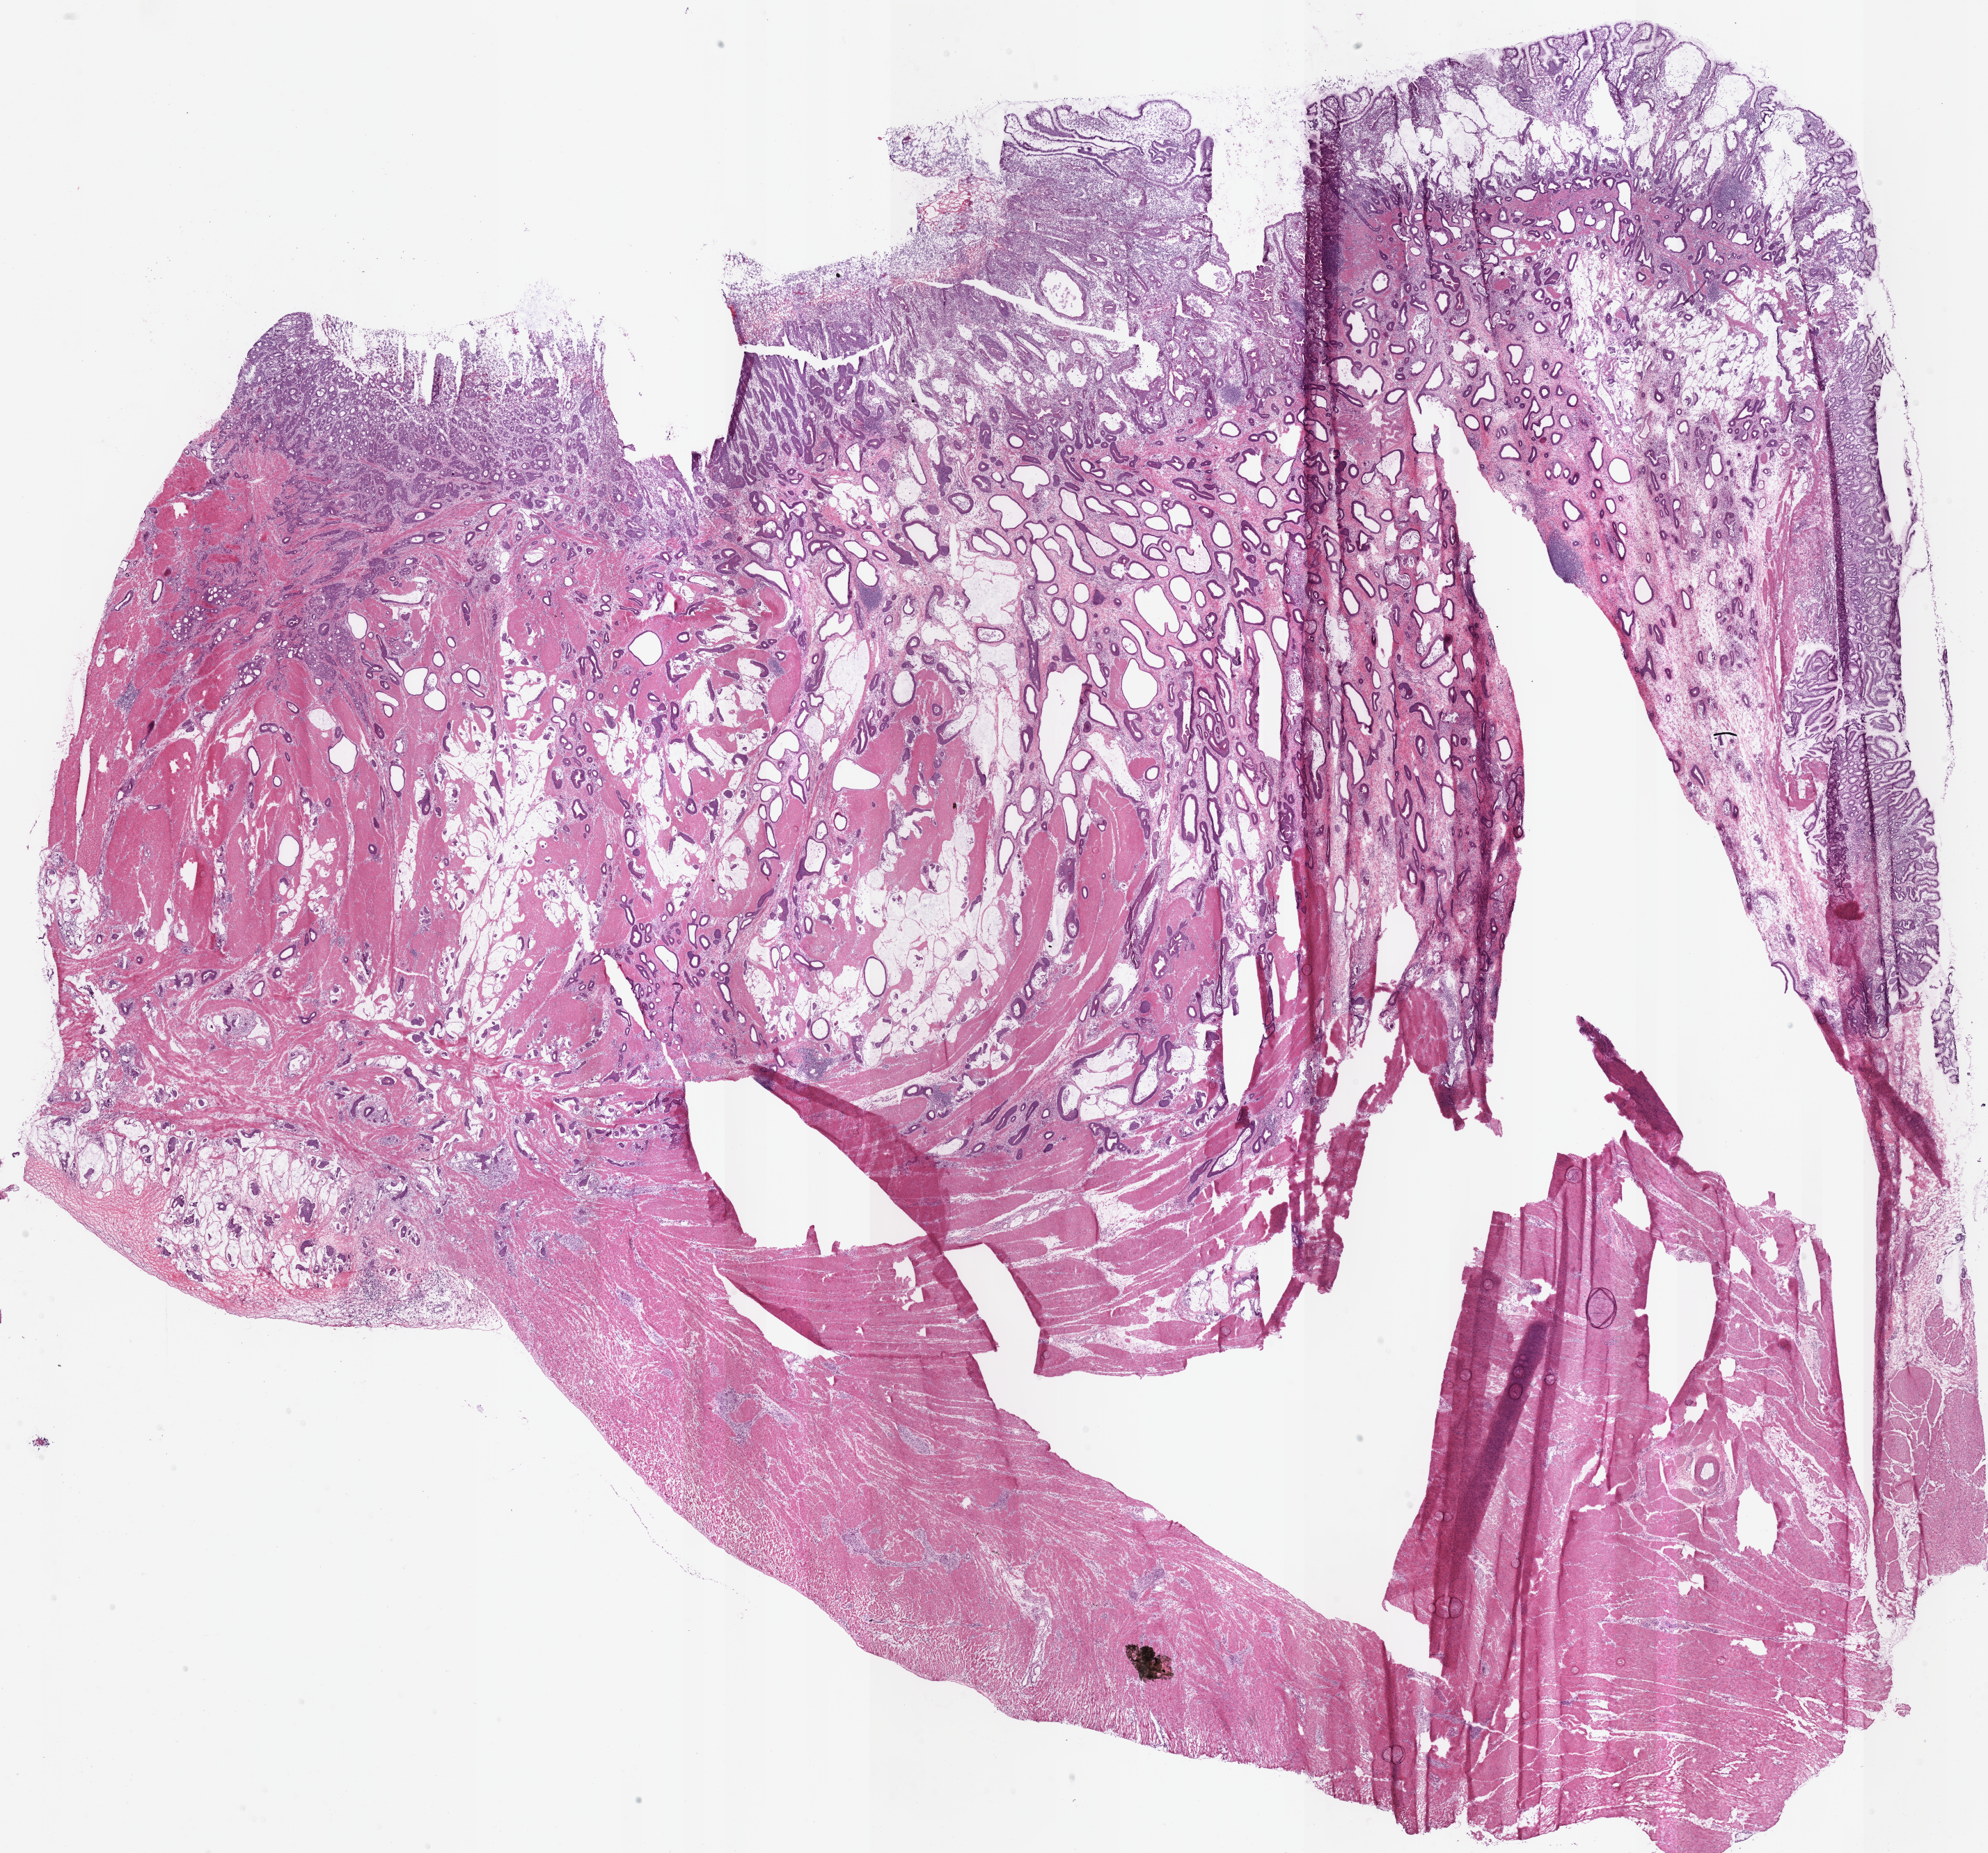
Digitized H&E tissue section (whole slide), low-resolution overview of the scanned area, about 22.5 x 21.0 mm. Frozen section. Stomach, primary tumour sample. Male patient; age at initial diagnosis 52 years.
Pathologic diagnosis: Mucinous adenocarcinoma.